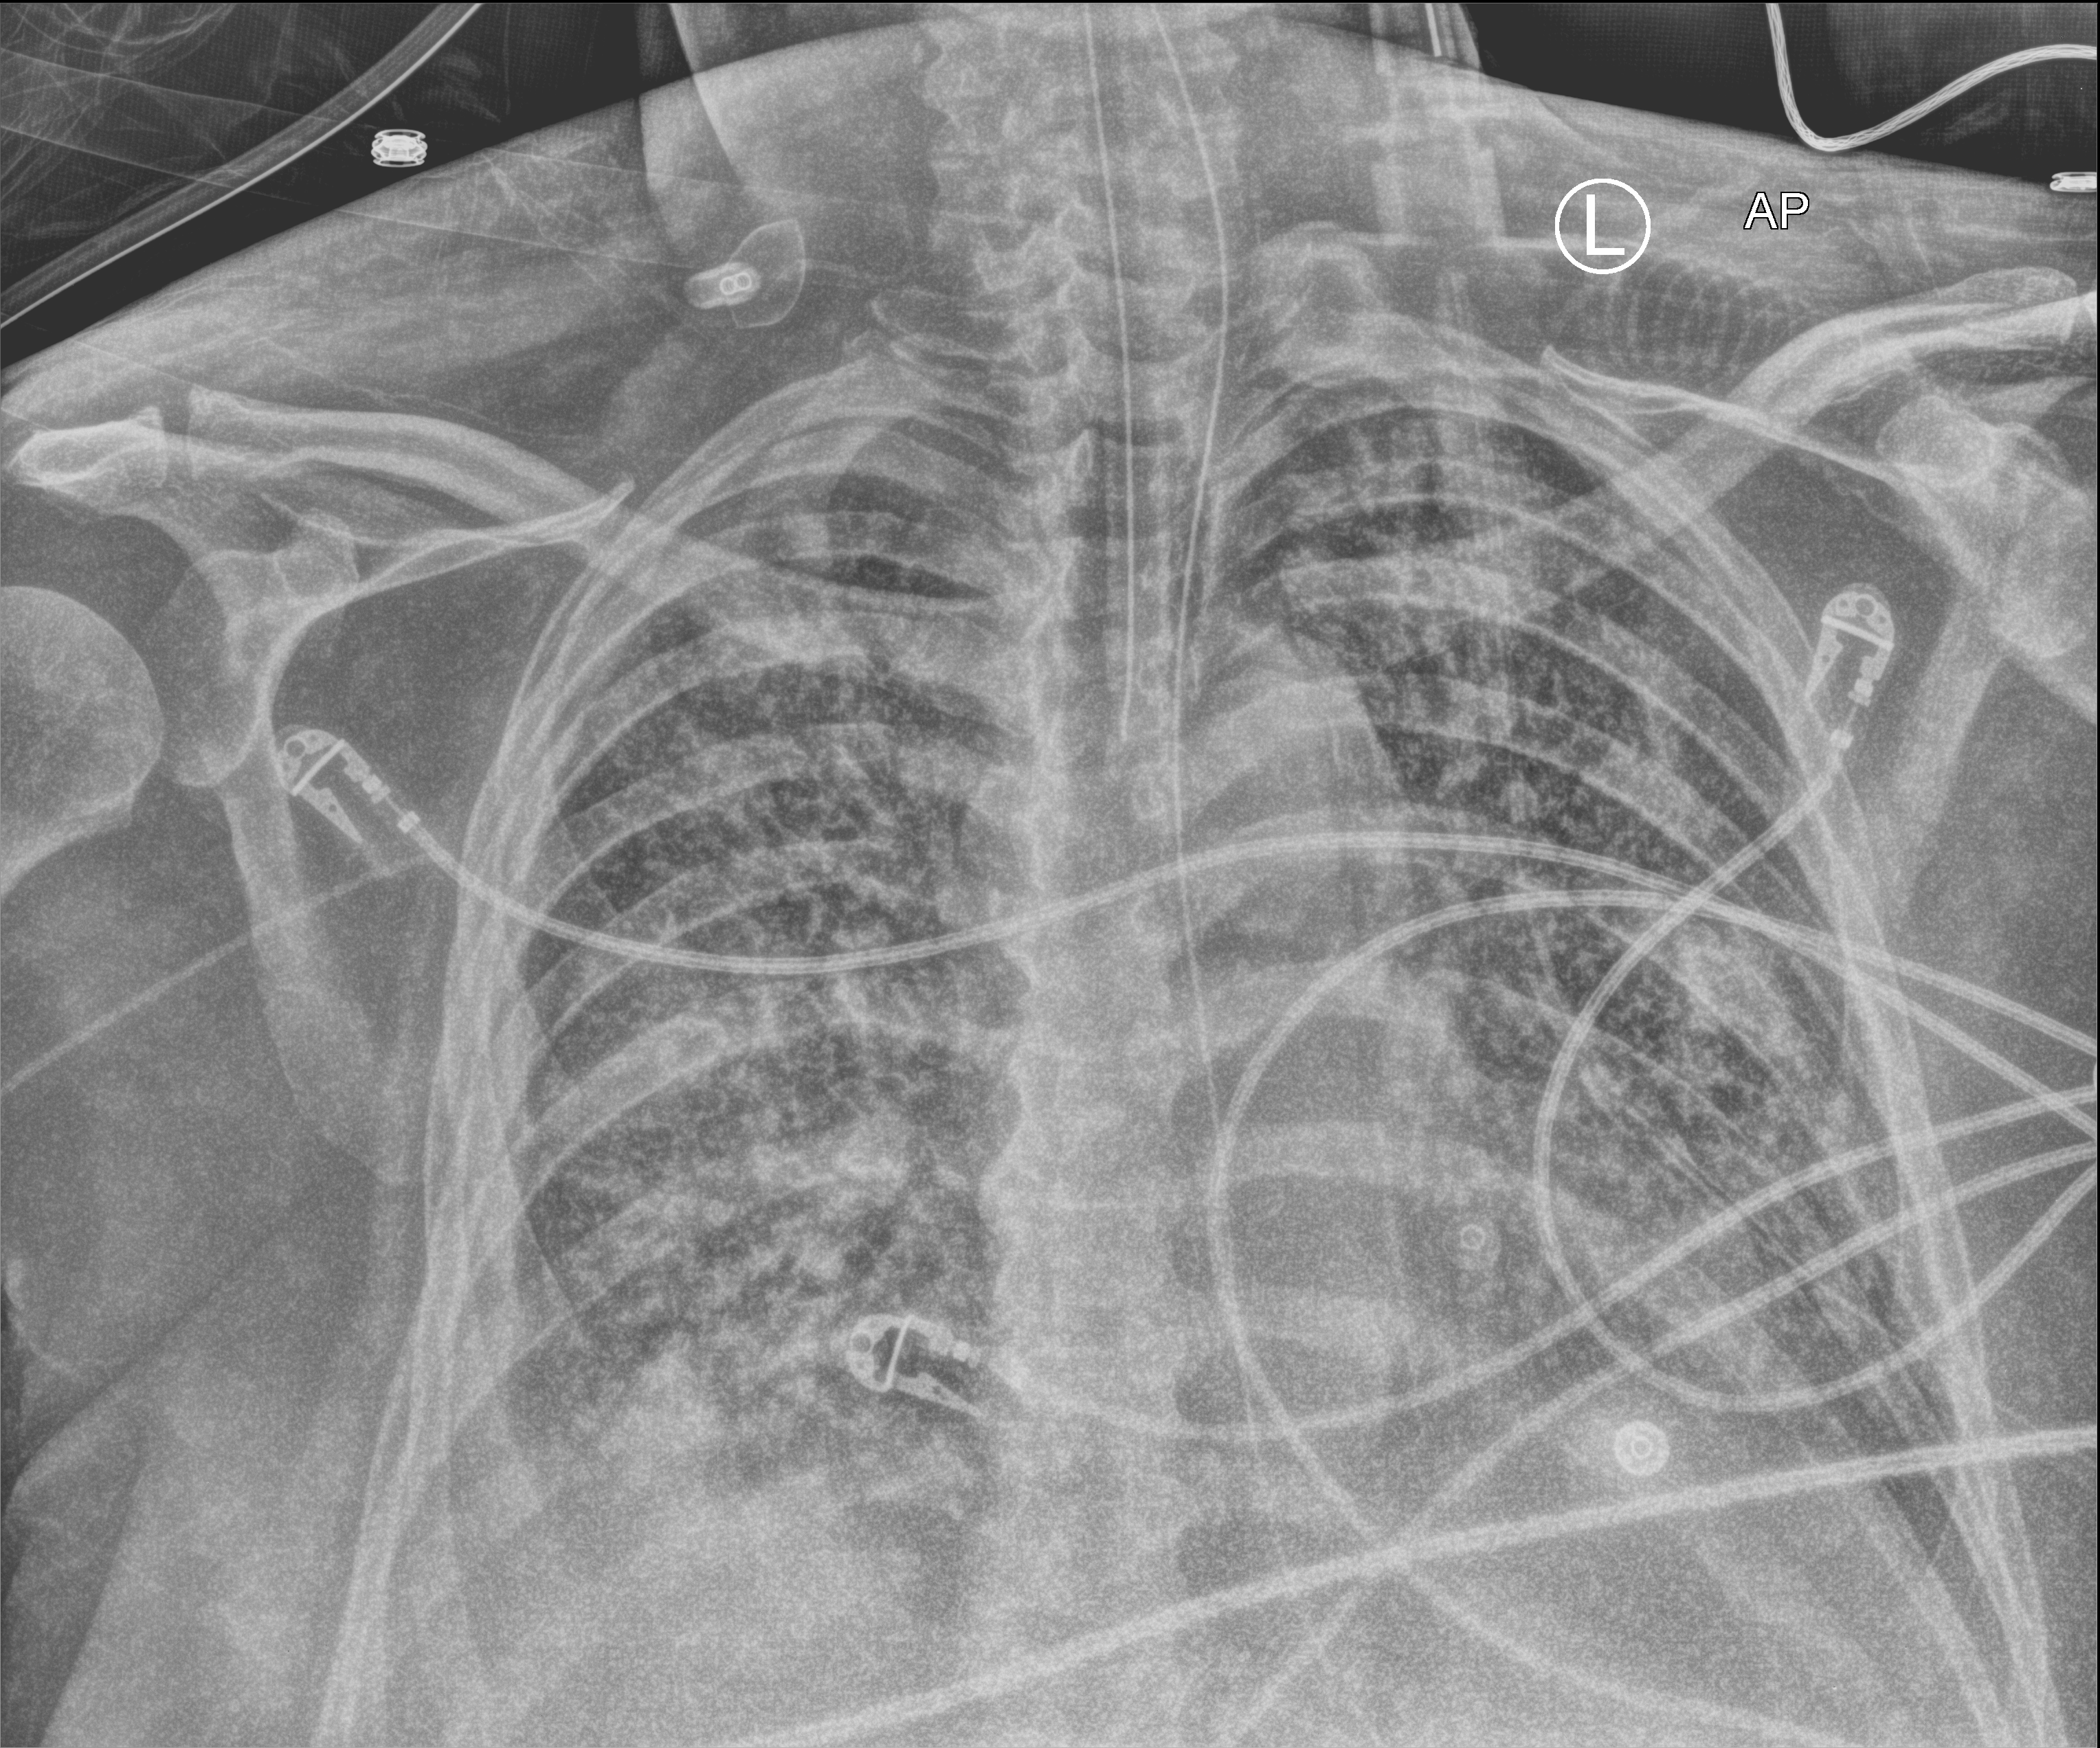
Chest X-ray (portable); anteroposterior (AP) projection. Patient hospitalised with COVID-19; male, aged 60–74 years.
Admission-level facts for this patient (not findings on this image; timing relative to this image not recorded): length of hospital stay: 40 days; admitted to intensive care during this hospital stay: yes; mechanically ventilated during this hospital stay: yes.